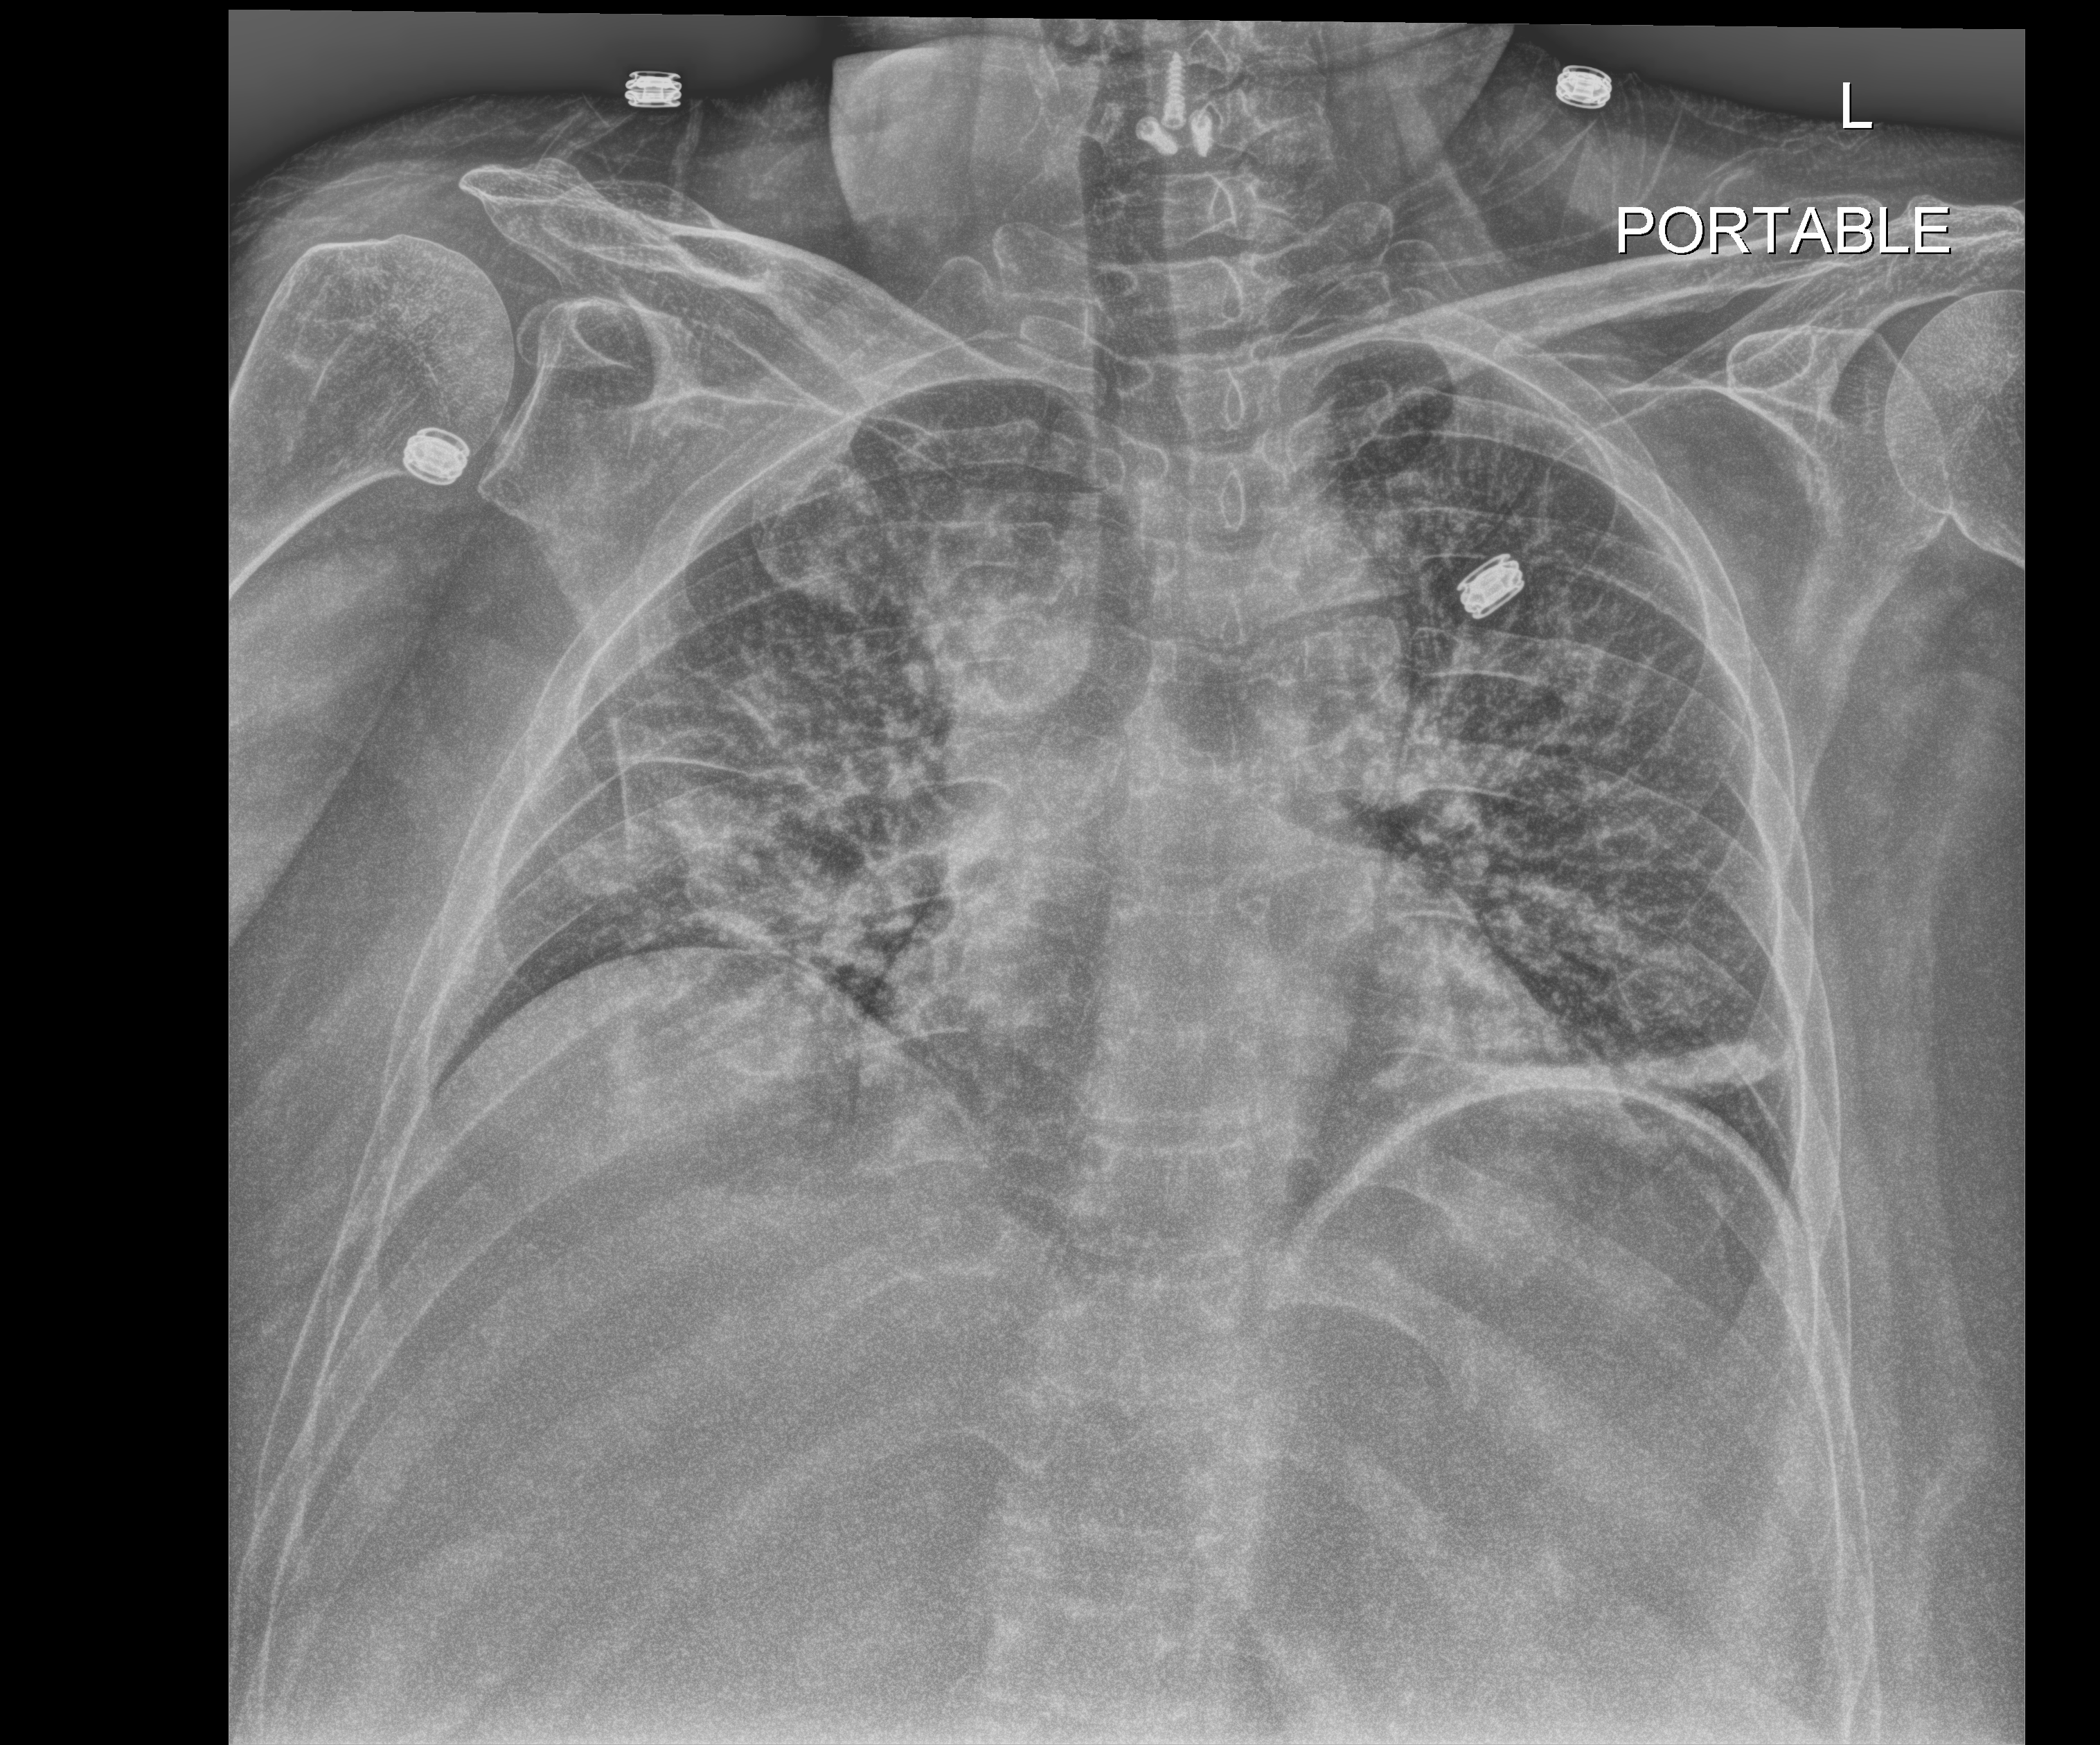
Chest radiograph. Patient hospitalised with COVID-19; female, aged 18–59 years.
From the hospital-stay record, not from the radiograph (when in the stay this image was taken is not recorded):
- mechanically ventilated during this hospital stay: no